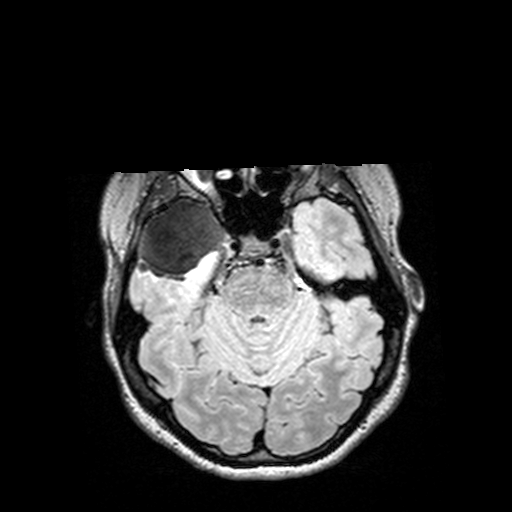
Brain MRI from a brain-tumour surgery series, one axial slice; position 100 of 144 along the scan axis; T2 FLAIR; 512 × 512 image matrix. From the clinical record (not read from this slice): histopathology: Astrocytoma; WHO grade: 3; IDH mutation: yes; tumour location: Right Insular Temporal.
Outlined on this slice (expert manual segmentation):
- tumour: bounding box <126,197,232,281> (left, top, right, bottom; pixels)